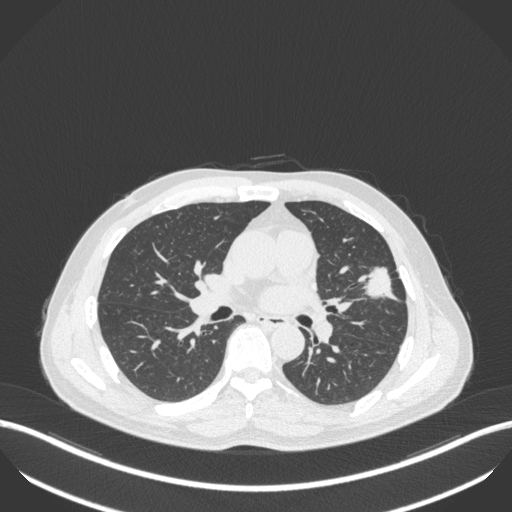
Chest CT, one axial slice. Slice 217 of 418 in the series (ordered by position). Reconstruction kernel B31f. 120 kVp. Lung window (W 1500 / L -600 HU). 1 mm slice thickness. 512 × 512 image matrix. Patient: male, 55 years. From the clinical record (not read from this slice): clinical TNM (as recorded): T1c N0 M0; histopathological grade: G2-3.
Structures marked on this image (rectangle marked by the reading radiologist):
- lung tumour (recorded histology: adenocarcinoma): box from (x=365, y=263) to (x=402, y=309) px